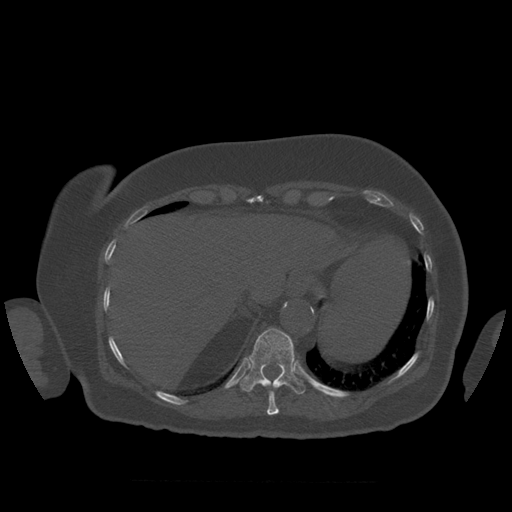
CT including the spine, one axial slice; slice 326 of 399 in the series (ordered by position); reconstruction kernel STANDARD; bone window (W 1800 / L 400 HU); 1.25 mm slice thickness; 512 × 512 image matrix, field of view 404 × 404 mm. Patient age 81 years. Case-level facts recorded for this patient, not image findings: primary cancer: renal.
Outlined on this slice (semi-automatic segmentation, software-assisted and operator-edited):
- T10 vertebra: box from (x=267, y=393) to (x=280, y=416) px
- T11 vertebra: (x=238, y=328)–(x=306, y=395)